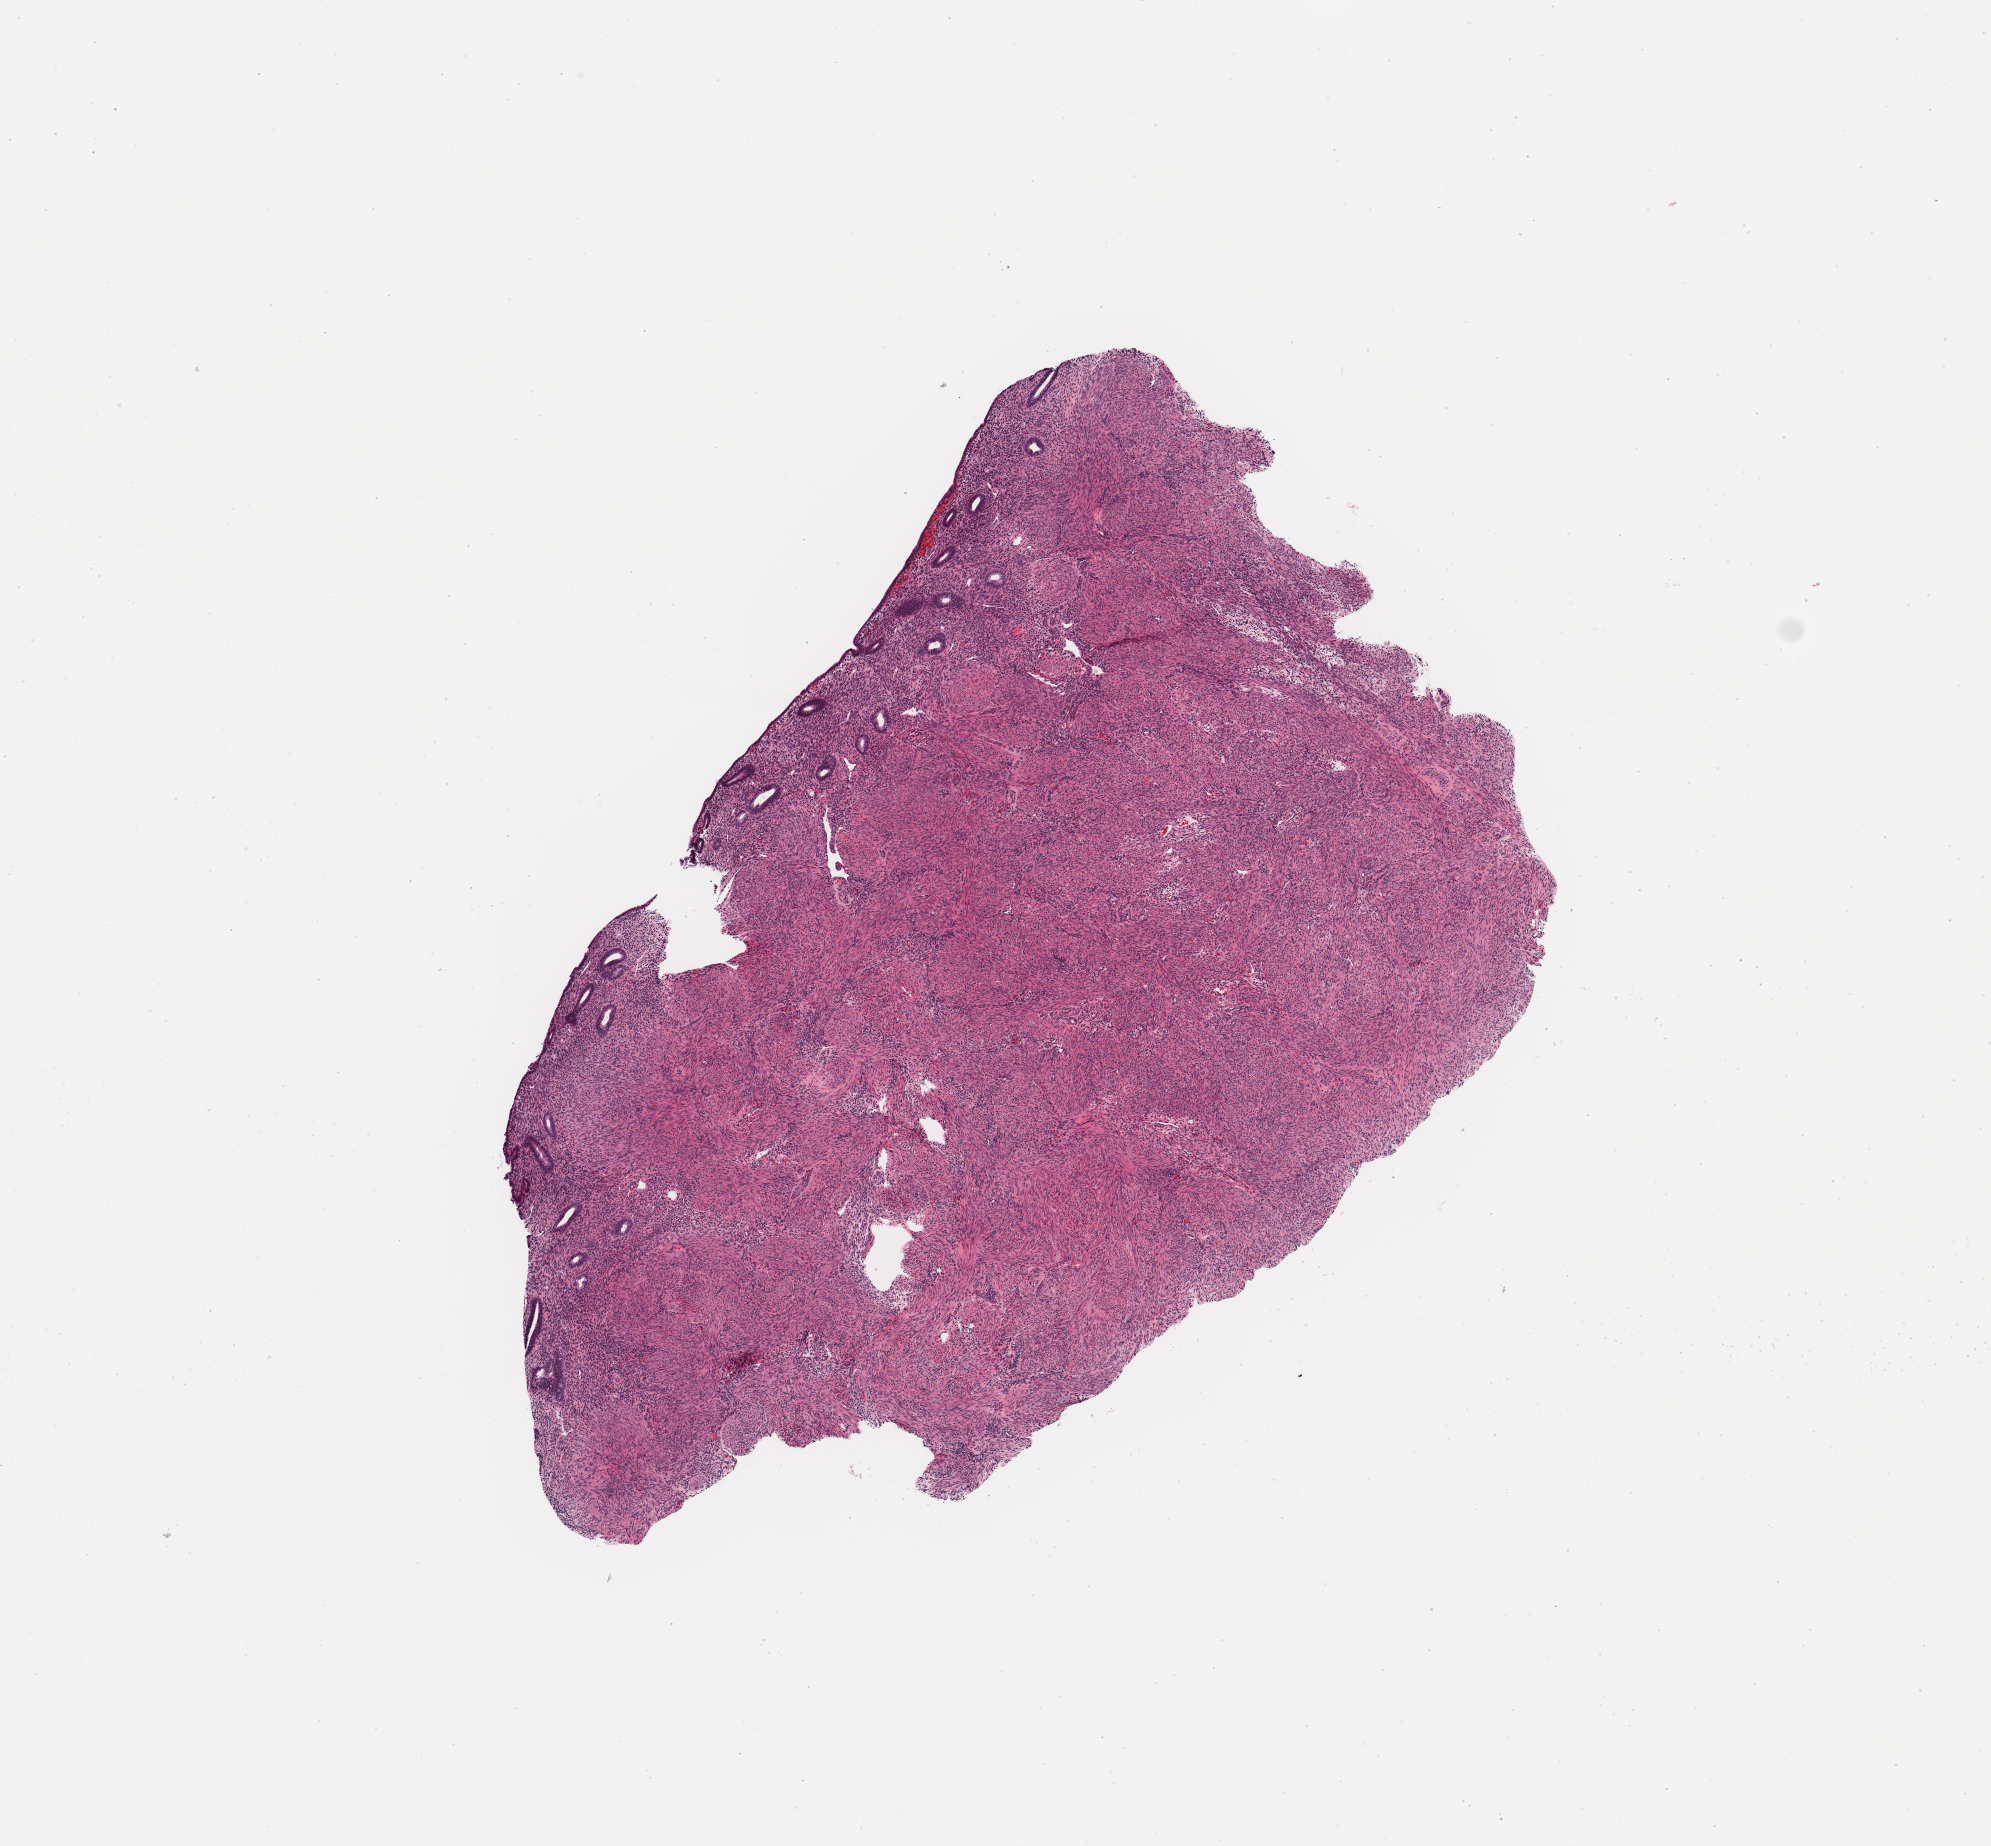
Whole-slide histology image, H&E — whole scanned area (about 7.9 x 7.3 mm, from a 20x scan) shown as a low-resolution overview. Normal (non-tumour) tissue sample, sampled site: uterus. Female, 80 y/o.
- this section: normal (non-tumour) tissue from the same patient
- patient diagnosis: Endometrioid adenocarcinoma, NOS